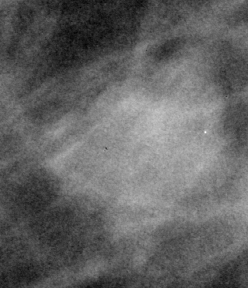
Crop from a digitized film mammogram around one marked abnormality, right breast, MLO view.
- Mass, shape irregular, margins microlobulated / ill defined; BI-RADS assessment category 4; pathology result (as recorded, not read from the image): benign.